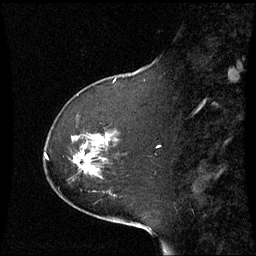
Breast MRI (dynamic contrast-enhanced), one sagittal slice. Slice 20 of 60 in the series (ordered by position). Dynamic contrast-enhanced series, image 2 of 3 at this slice position (ordered by acquisition). 1.5 T. TE 4.2 ms, TR 8.9 ms. 2.4 mm slice thickness. 256 × 256 image matrix. Female patient, age 51 years. From the clinical record (not read from this slice): setting: breast cancer imaged before/during neoadjuvant chemotherapy; receptor status: HR-positive, HER2-negative.
Outlined on this slice (semi-automatically segmented with operator editing):
- analysis volume of interest (the breast-tissue region the enhancement analysis was run in; not a lesion): bounding box [x1, y1, x2, y2] px = [45, 132, 114, 192]
- tumour enhancement mask (voxels above the 70 % enhancement threshold inside the analysis volume of interest): [74, 136, 102, 172]